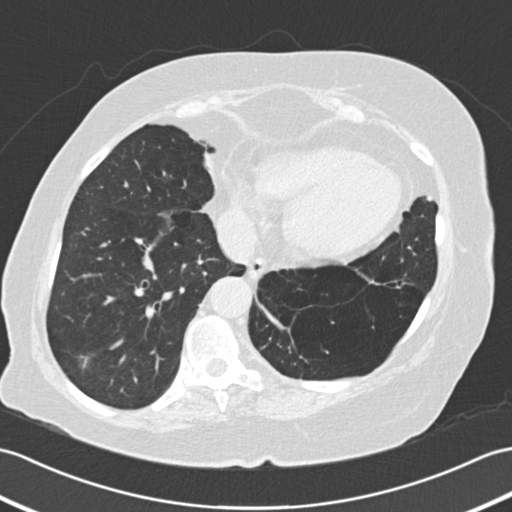
Low-dose screening chest CT, one axial slice. Position 56 of 161 along the scan axis. Reconstruction kernel B30f. 120 kVp. Lung window (W 1500 / L -600 HU). 2 mm slice thickness. 512 × 512 image matrix.
Outlined on this slice (expert manual segmentation):
- lesion 1 (tumor, lower lobe of right lung): bounding box <81,356,88,368> (left, top, right, bottom; pixels)